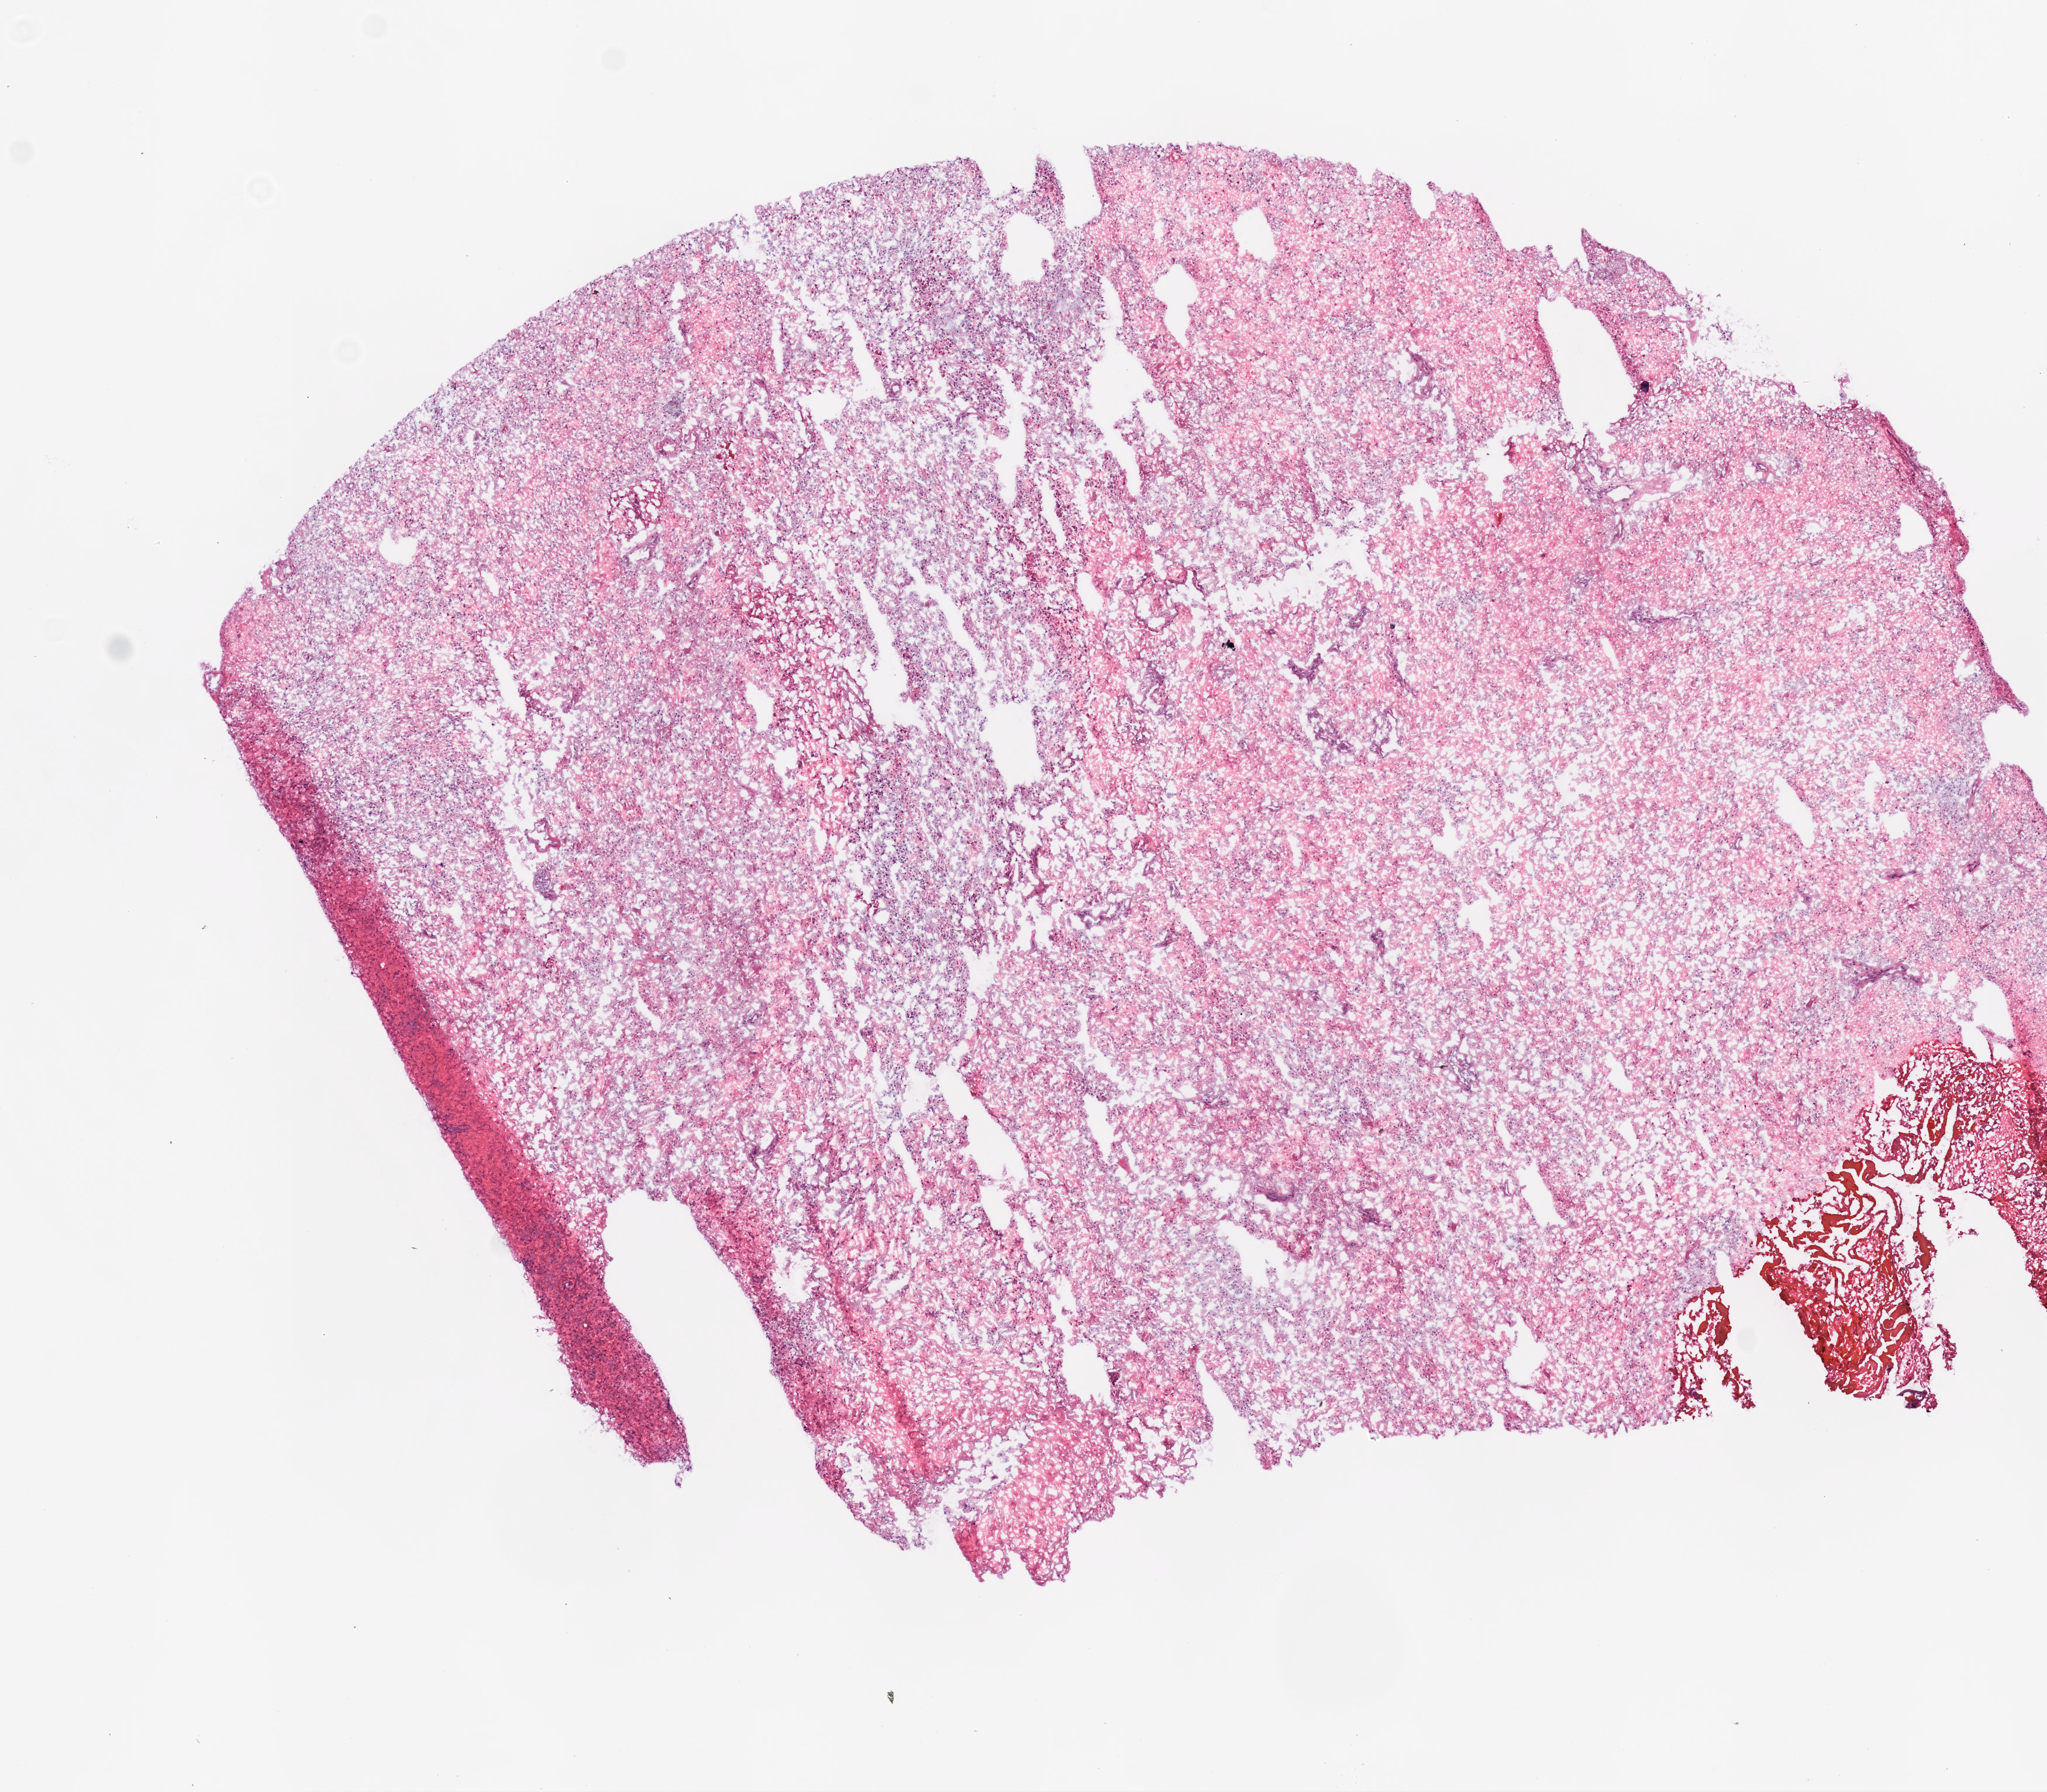
Whole-slide histology image, Hematoxylin and eosin (H&E) stained, a low-resolution overview of the entire scanned area, about 7.0 x 6.1 mm; frozen section from the top of the tissue portion; brain, primary tumour sample. Male, age 89 years at initial diagnosis. Slide review estimates, as recorded: tumour cells 100%, tumour nuclei 80%, normal cells 0%, stromal cells 0%, necrosis 0%.
* pathologic diagnosis: Glioblastoma